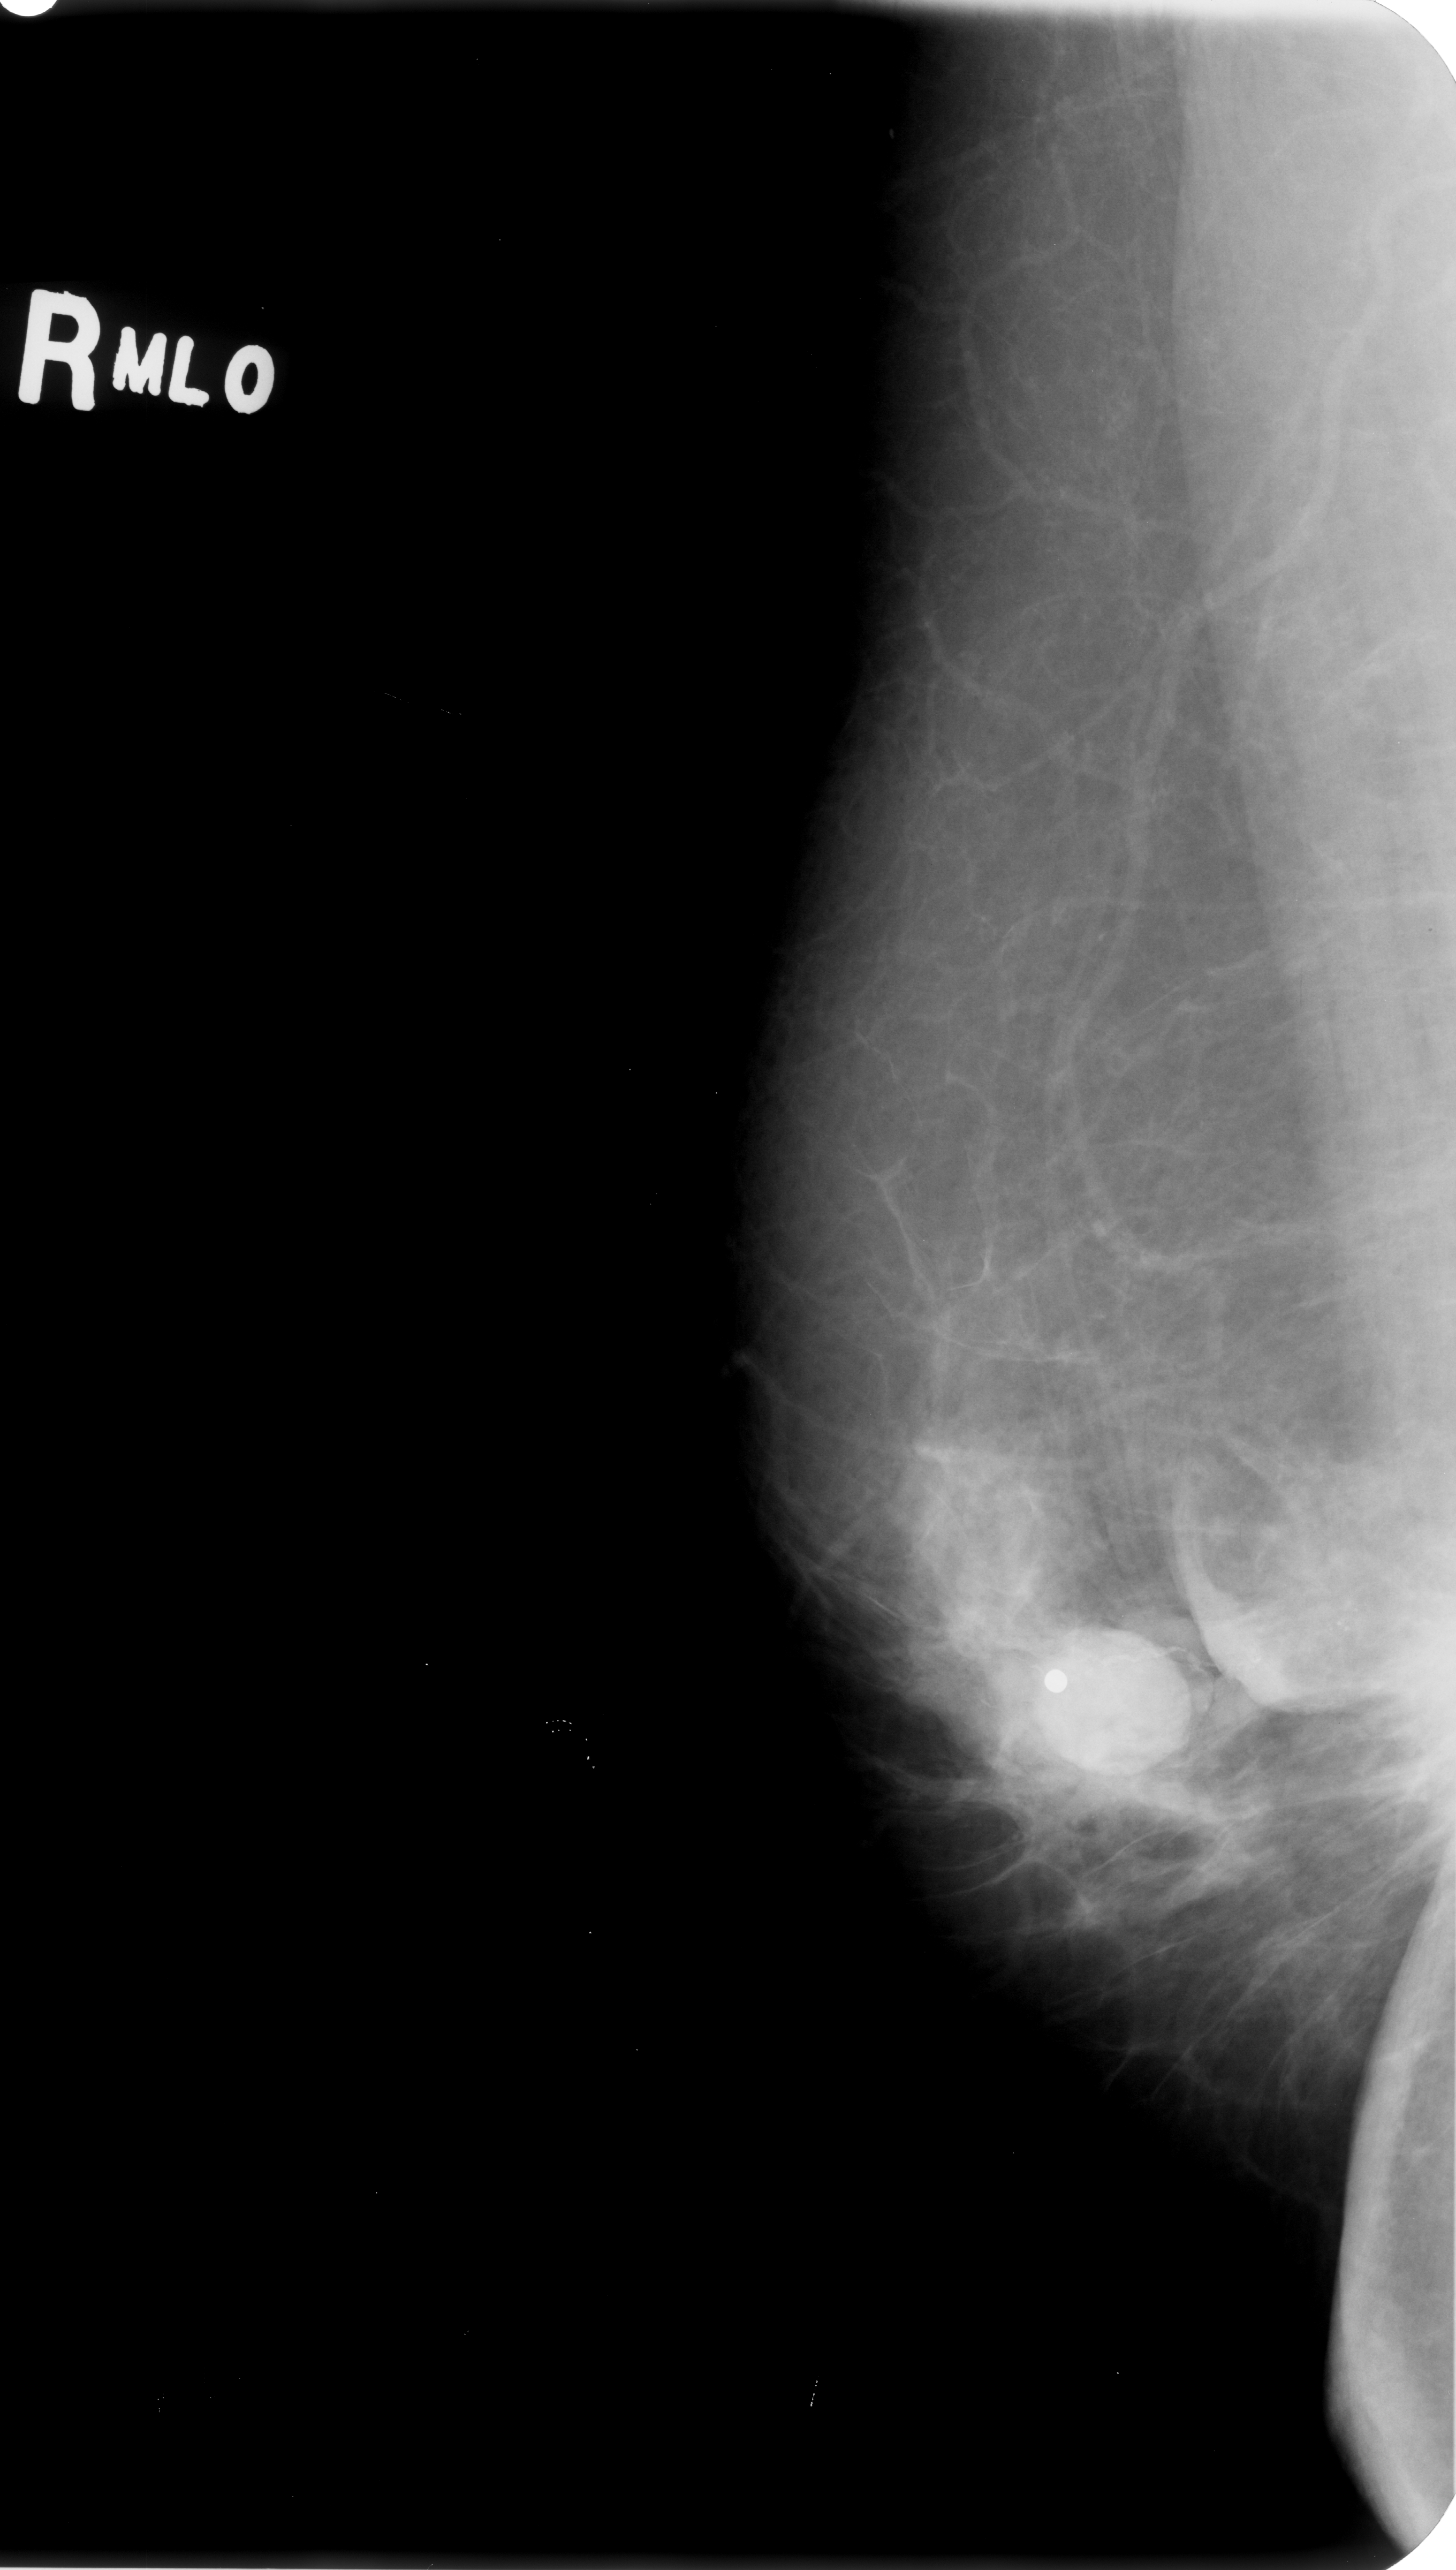
Mammogram (digitized film); right breast; MLO view; breast composition: scattered fibroglandular densities (BI-RADS density category 2 of 4); 1456 × 2570 image matrix.
Expert-marked regions of interest on this film, with their recorded descriptors:
- mass, shape irregular, margins spiculated; BI-RADS assessment category 5; subtlety rating 5 on a 1 (subtle) to 5 (obvious) scale; pathology result (as recorded, not read from the image): malignant: box from (x=1354, y=1643) to (x=1456, y=1818) px